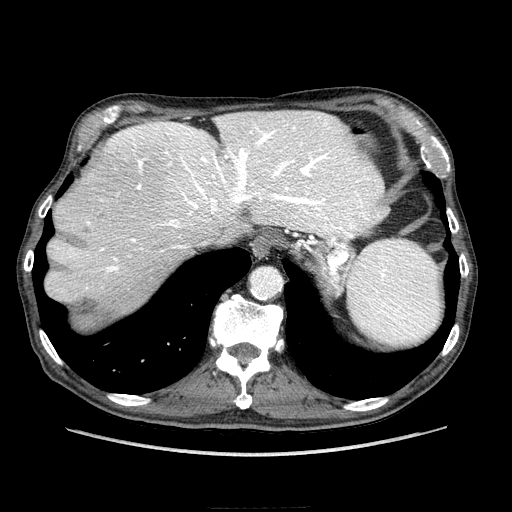
Contrast-enhanced abdominal CT (liver protocol), one axial slice; slice 179 of 218 in the series (ordered by position); reconstruction kernel STANDARD; 100 kVp; soft-tissue window (W 400 / L 40 HU); 2.5 mm slice thickness; 512 × 512 image matrix, field of view 380 × 380 mm. Case-level facts recorded for this patient, not image findings: diagnosis: hepatocellular carcinoma (patient treated with transarterial chemoembolisation; whether this scan precedes or follows treatment is not stated here); TNM stage (as recorded): Stage-IIIA; Child-Pugh class: A; tumour differentiation: well differentiated; tumour nodularity: multinodular.
Structures marked on this image (semi-automatically segmented with operator editing):
- abdominal aorta: bounding box (x1, y1, x2, y2) in pixels: (250, 269, 280, 296)
- liver parenchyma outside the tumour (the mass and vessels are separate outlines, so this box may not span the whole liver): (48, 110, 382, 314)
- liver vessels: (56, 112, 381, 289)